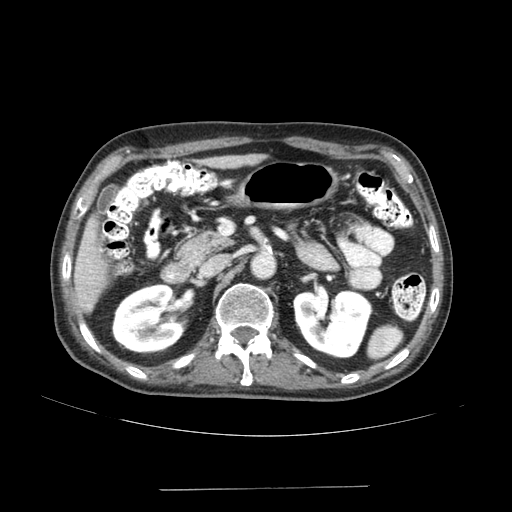
Contrast-enhanced abdominal CT (liver protocol), one axial slice. Position 68 of 192 along the scan axis. Reconstruction kernel SOFT. 120 kVp. Soft-tissue window (W 400 / L 40 HU). 512 × 512 image matrix, field of view 400 × 400 mm. From the clinical record (not read from this slice): diagnosis: hepatocellular carcinoma (patient treated with transarterial chemoembolisation; whether this scan precedes or follows treatment is not stated here); TNM stage (as recorded): Stage-IVA; Child-Pugh class: A; tumour differentiation: poorly differentiated; tumour nodularity: uninodular.
Structures marked on this image (semi-automatic segmentation, software-assisted and operator-edited):
- liver parenchyma outside the tumour (the mass and vessels are separate outlines, so this box may not span the whole liver): bounding box (x1, y1, x2, y2) in pixels: (74, 154, 260, 312)